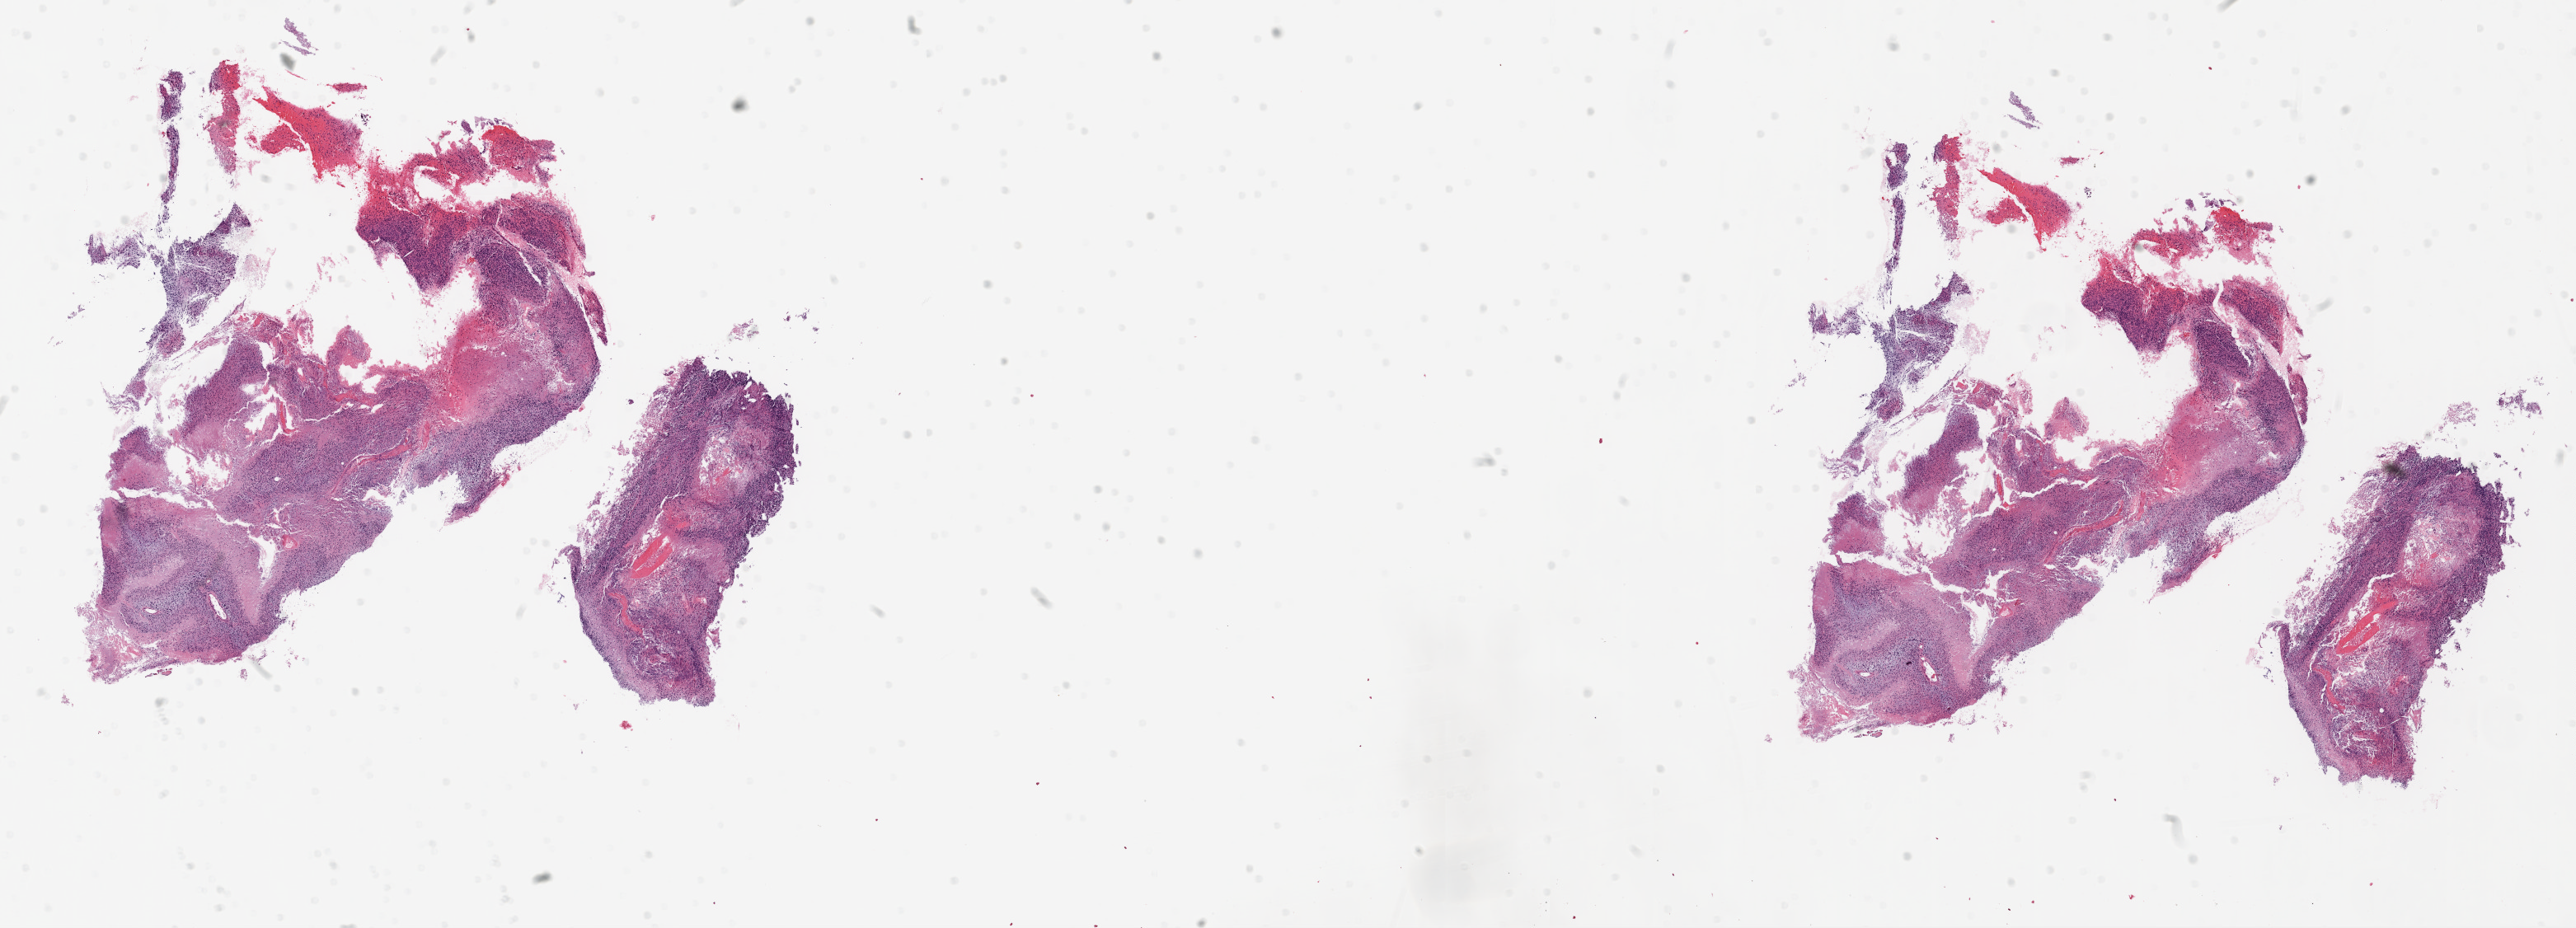
Digitized Hematoxylin and eosin (H&E) stained tissue section (whole slide), whole scanned area (about 25.1 x 9.0 mm) shown as a low-resolution overview; formalin-fixed paraffin-embedded (FFPE) diagnostic section; sample: primary tumour, brain. Patient: male, age at initial diagnosis 70 years.
Histologic diagnosis: Glioblastoma.